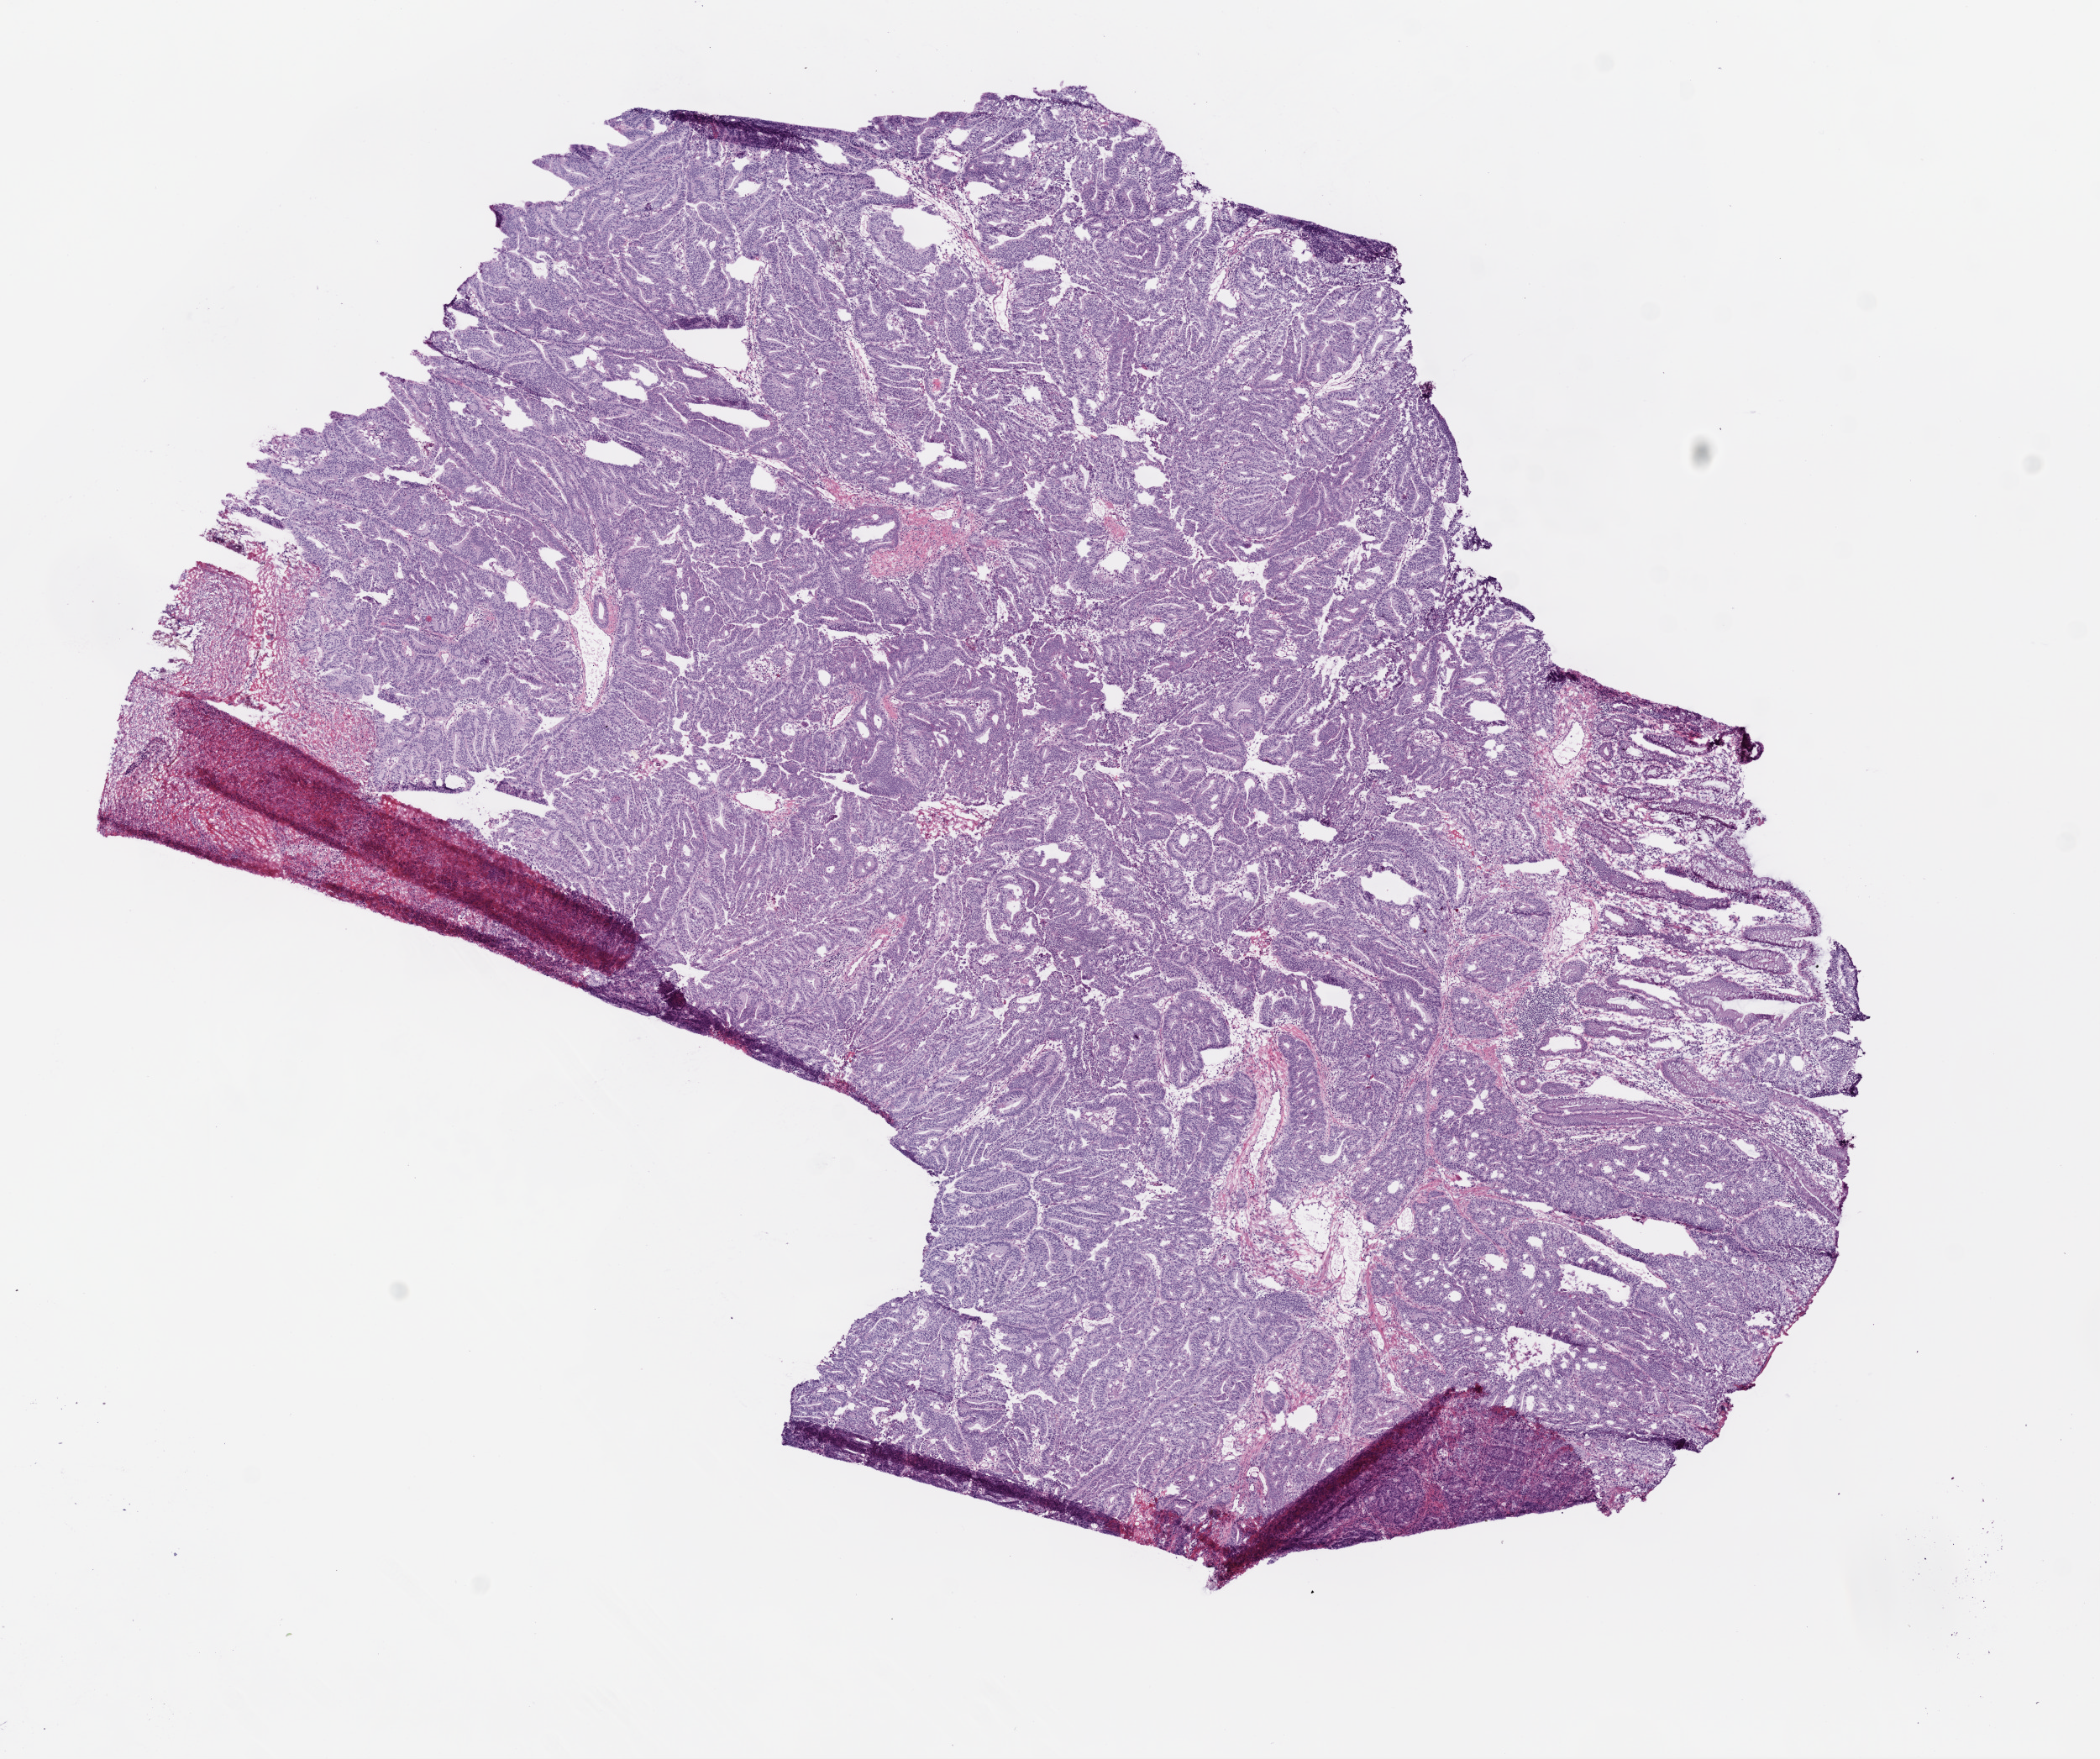
H&E whole-slide image — a low-resolution overview of the entire scanned area, about 10.0 x 8.4 mm (acquisition: 20x scan). Frozen section from the top of the tissue portion. Sample: primary tumour, rectum. Female patient; age at initial diagnosis 85 years. Slide review estimates, as recorded: tumour cells 90%, tumour nuclei 97%.
Histologic diagnosis: Adenocarcinoma, NOS (rectosigmoid junction).